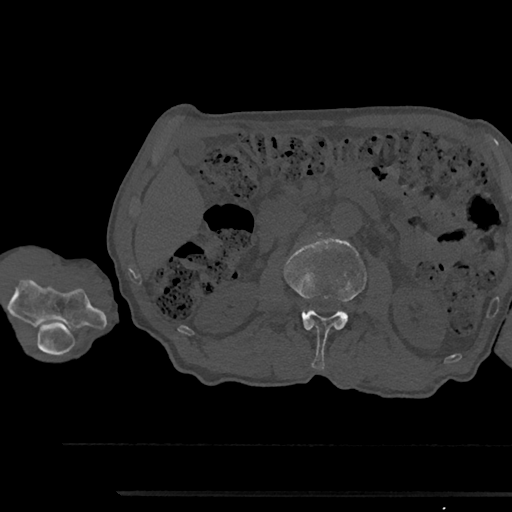
CT including the spine, one axial slice. Position 554 of 797 along the scan axis. 120 kVp. Bone window (W 1800 / L 400 HU). 0.5 mm slice thickness. 512 × 512 image matrix. Patient: male, 79 years. From the clinical record (not read from this slice): primary cancer: prostate.
Annotated regions visible in this slice (semi-automatically segmented with operator editing):
- L2 vertebra: bounding box (x1, y1, x2, y2) in pixels: (284, 234, 367, 369)